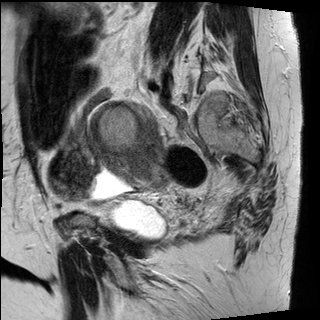
Pelvic MRI for cervical cancer, one sagittal slice; position 22 of 30 along the scan axis; T2-weighted; 1.5 T; TE 89 ms, TR 2930 ms; 320 × 320 image matrix, field of view 260 × 260 mm. Patient: female, 62 years.
Annotated regions visible in this slice (outlined manually by an expert reader):
- uterus and cervix: box from (x=89, y=99) to (x=172, y=188) px